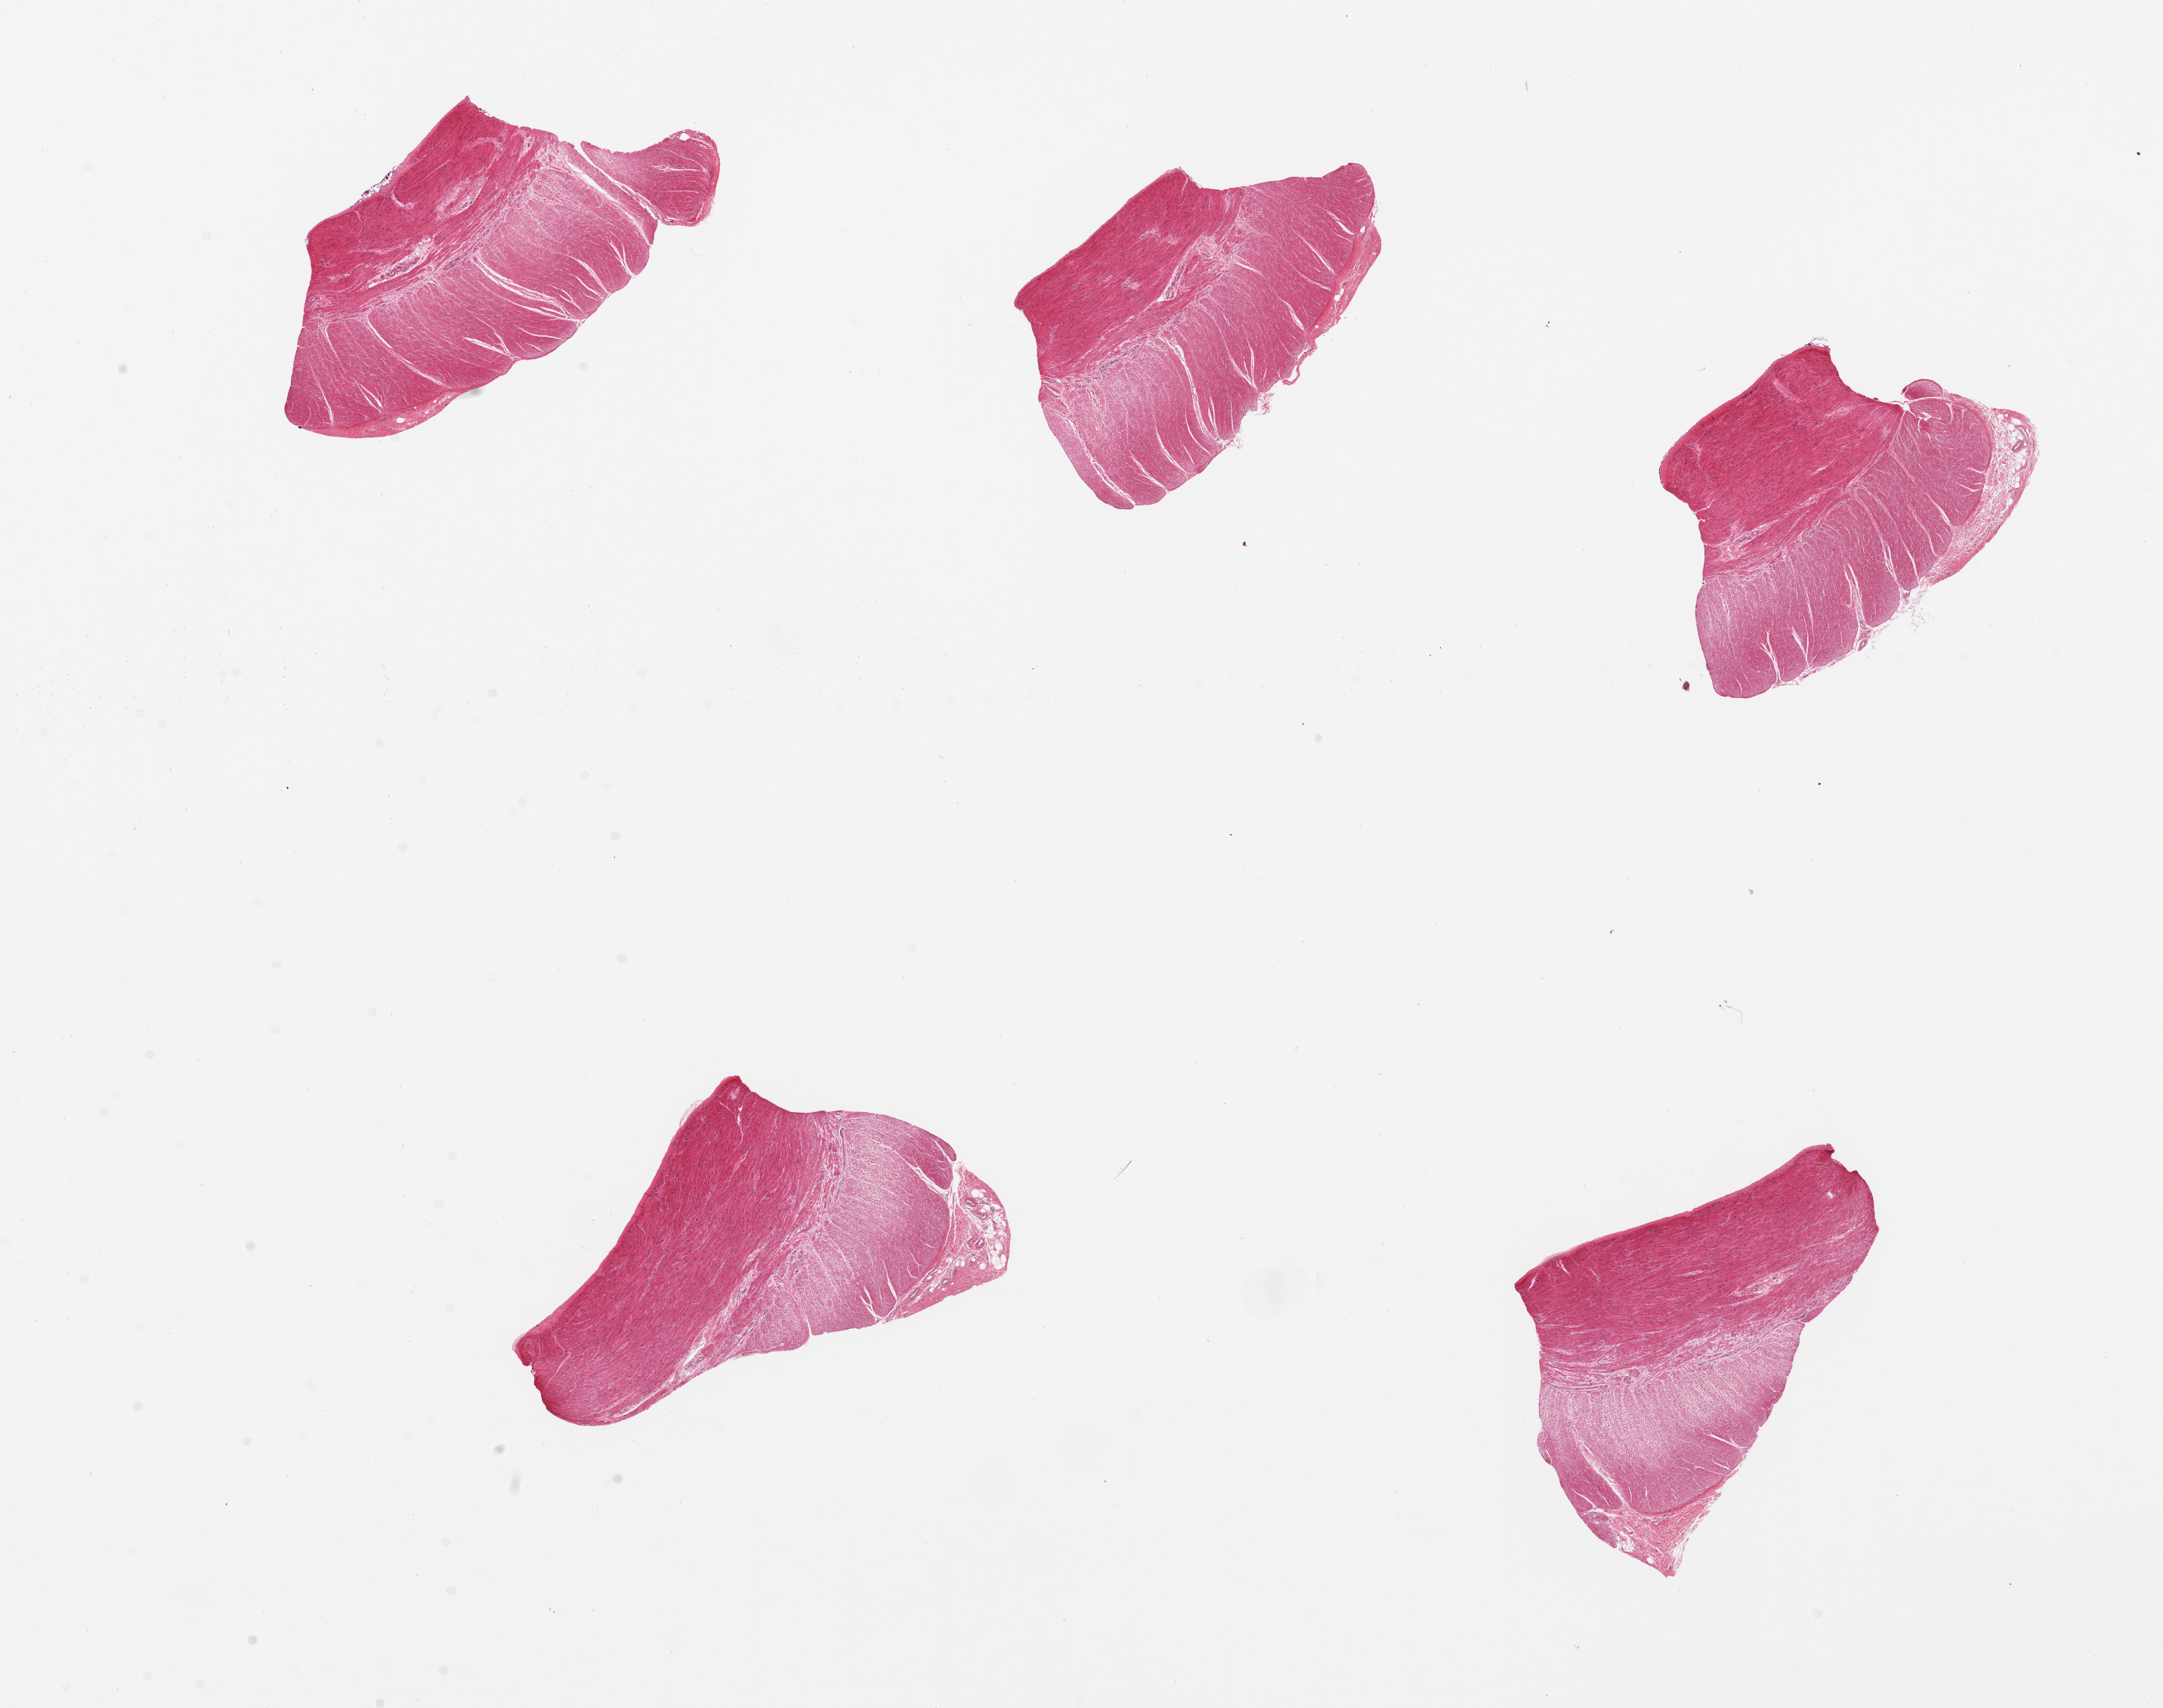
Digitized hematoxylin and eosin (H&E)-stained section — whole scanned area (about 22.6 x 17.9 mm) shown as a low-resolution overview, PAXgene-fixed paraffin-embedded (PFPE) section, sampled site (target tissue): sigmoid colon, tissue donor sample. Female donor.
Pathologist's review note for this sample: 5 pieces, well trimmed.